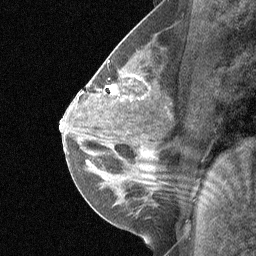
Breast MRI (dynamic contrast-enhanced), one sagittal slice; slice 34 of 64 in the series (ordered by position); dynamic contrast-enhanced study with each time point stored as its own series, time point 3 of 5 at this slice position (ordered by acquisition time); 1.5 T; TE 4.8 ms, TR 27 ms; 256 × 256 image matrix. Patient: female, 26 years. From the clinical record (not read from this slice): setting: breast cancer imaged before/during neoadjuvant chemotherapy; receptor status: HR-positive, HER2-negative.
Outlined on this slice (semi-automatic segmentation, software-assisted and operator-edited):
- analysis volume of interest (the breast-tissue region the enhancement analysis was run in; not a lesion): box from (x=85, y=46) to (x=171, y=144) px
- tumour enhancement mask (voxels above the 90 % enhancement threshold inside the analysis volume of interest): (x=110, y=85)–(x=117, y=92)